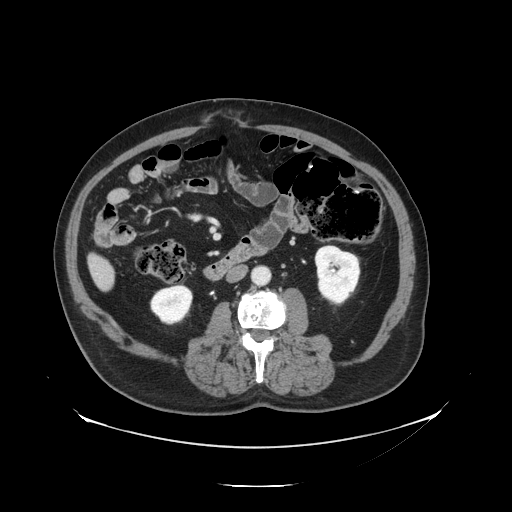
Contrast-enhanced abdominal CT, one axial slice. Slice 34 of 138 in the series (ordered by position). Reconstruction kernel STANDARD. 120 kVp. Intravenous contrast given. Soft-tissue window (W 400 / L 40 HU). 2.5 mm slice thickness. 512 × 512 image matrix. Male patient, age 77 years. From the clinical record (not read from this slice): diagnosis: colorectal cancer liver metastases, imaged before liver resection; multiple liver metastases: no; largest metastasis: 1.5 cm.
Annotated regions visible in this slice (expert manual segmentation):
- liver: bounding box (x1, y1, x2, y2) in pixels: (91, 256, 114, 289)
- planned liver remnant (the part of the liver to remain after resection): (90, 256, 110, 274)